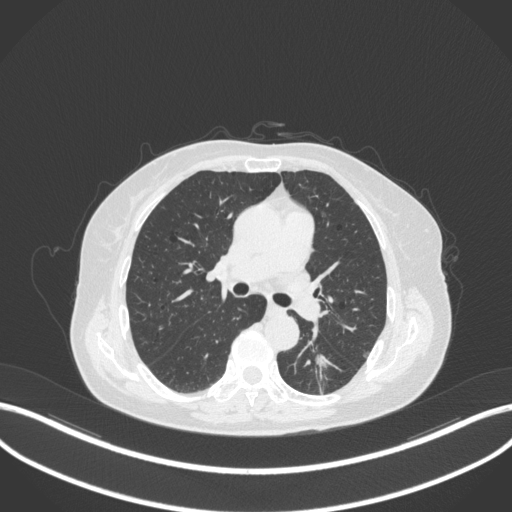
Chest CT, one axial slice; slice 175 of 352 in the series (ordered by position); 120 kVp; lung window (W 1500 / L -600 HU); 1 mm slice thickness; 512 × 512 image matrix. Female patient, age 70 years. From the clinical record (not read from this slice): clinical TNM (as recorded): T1c N0 M0.
Structures marked on this image (bounding box drawn by a radiologist):
- lung tumour (recorded histology: adenocarcinoma): bounding box [x1, y1, x2, y2] px = [310, 346, 343, 393]